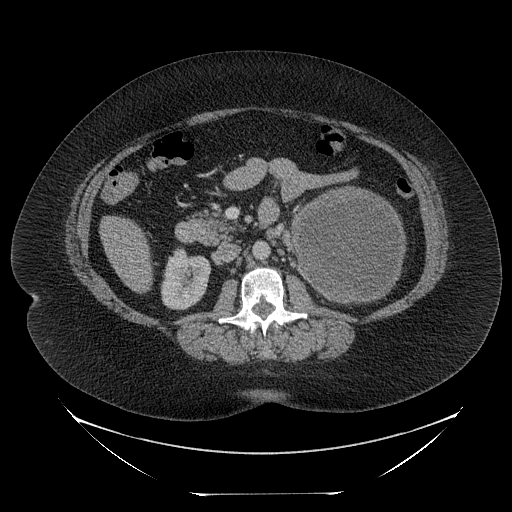
Contrast-enhanced abdominal CT, one axial slice. Position 123 of 205 along the scan axis. Reconstruction kernel STANDARD. 120 kVp. Intravenous contrast given. Soft-tissue window (W 400 / L 40 HU). 512 × 512 image matrix, field of view 500 × 500 mm. Female patient, age 53 years. Case-level facts recorded for this patient, not image findings: diagnosis: adrenocortical carcinoma; tumour side: left adrenal; tumour size at pathology: 17 cm; Ki-67 index: 20 %; stage (as recorded): 3.
Outlined on this slice (semi-automatic segmentation, software-assisted and operator-edited):
- mass: bounding box (x1, y1, x2, y2) in pixels: (295, 190, 403, 300)